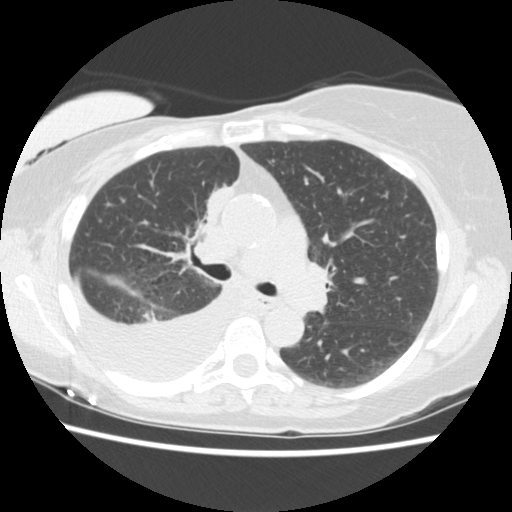
Low-dose screening chest CT, one axial slice; position 93 of 157 along the scan axis; reconstruction kernel STANDARD; 120 kVp; lung window (W 1500 / L -600 HU); 512 × 512 image matrix.
Annotated regions visible in this slice (expert manual segmentation):
- lesion 1 (tumor, upper lobe of right lung): bounding box (x1, y1, x2, y2) in pixels: (205, 185, 233, 222)